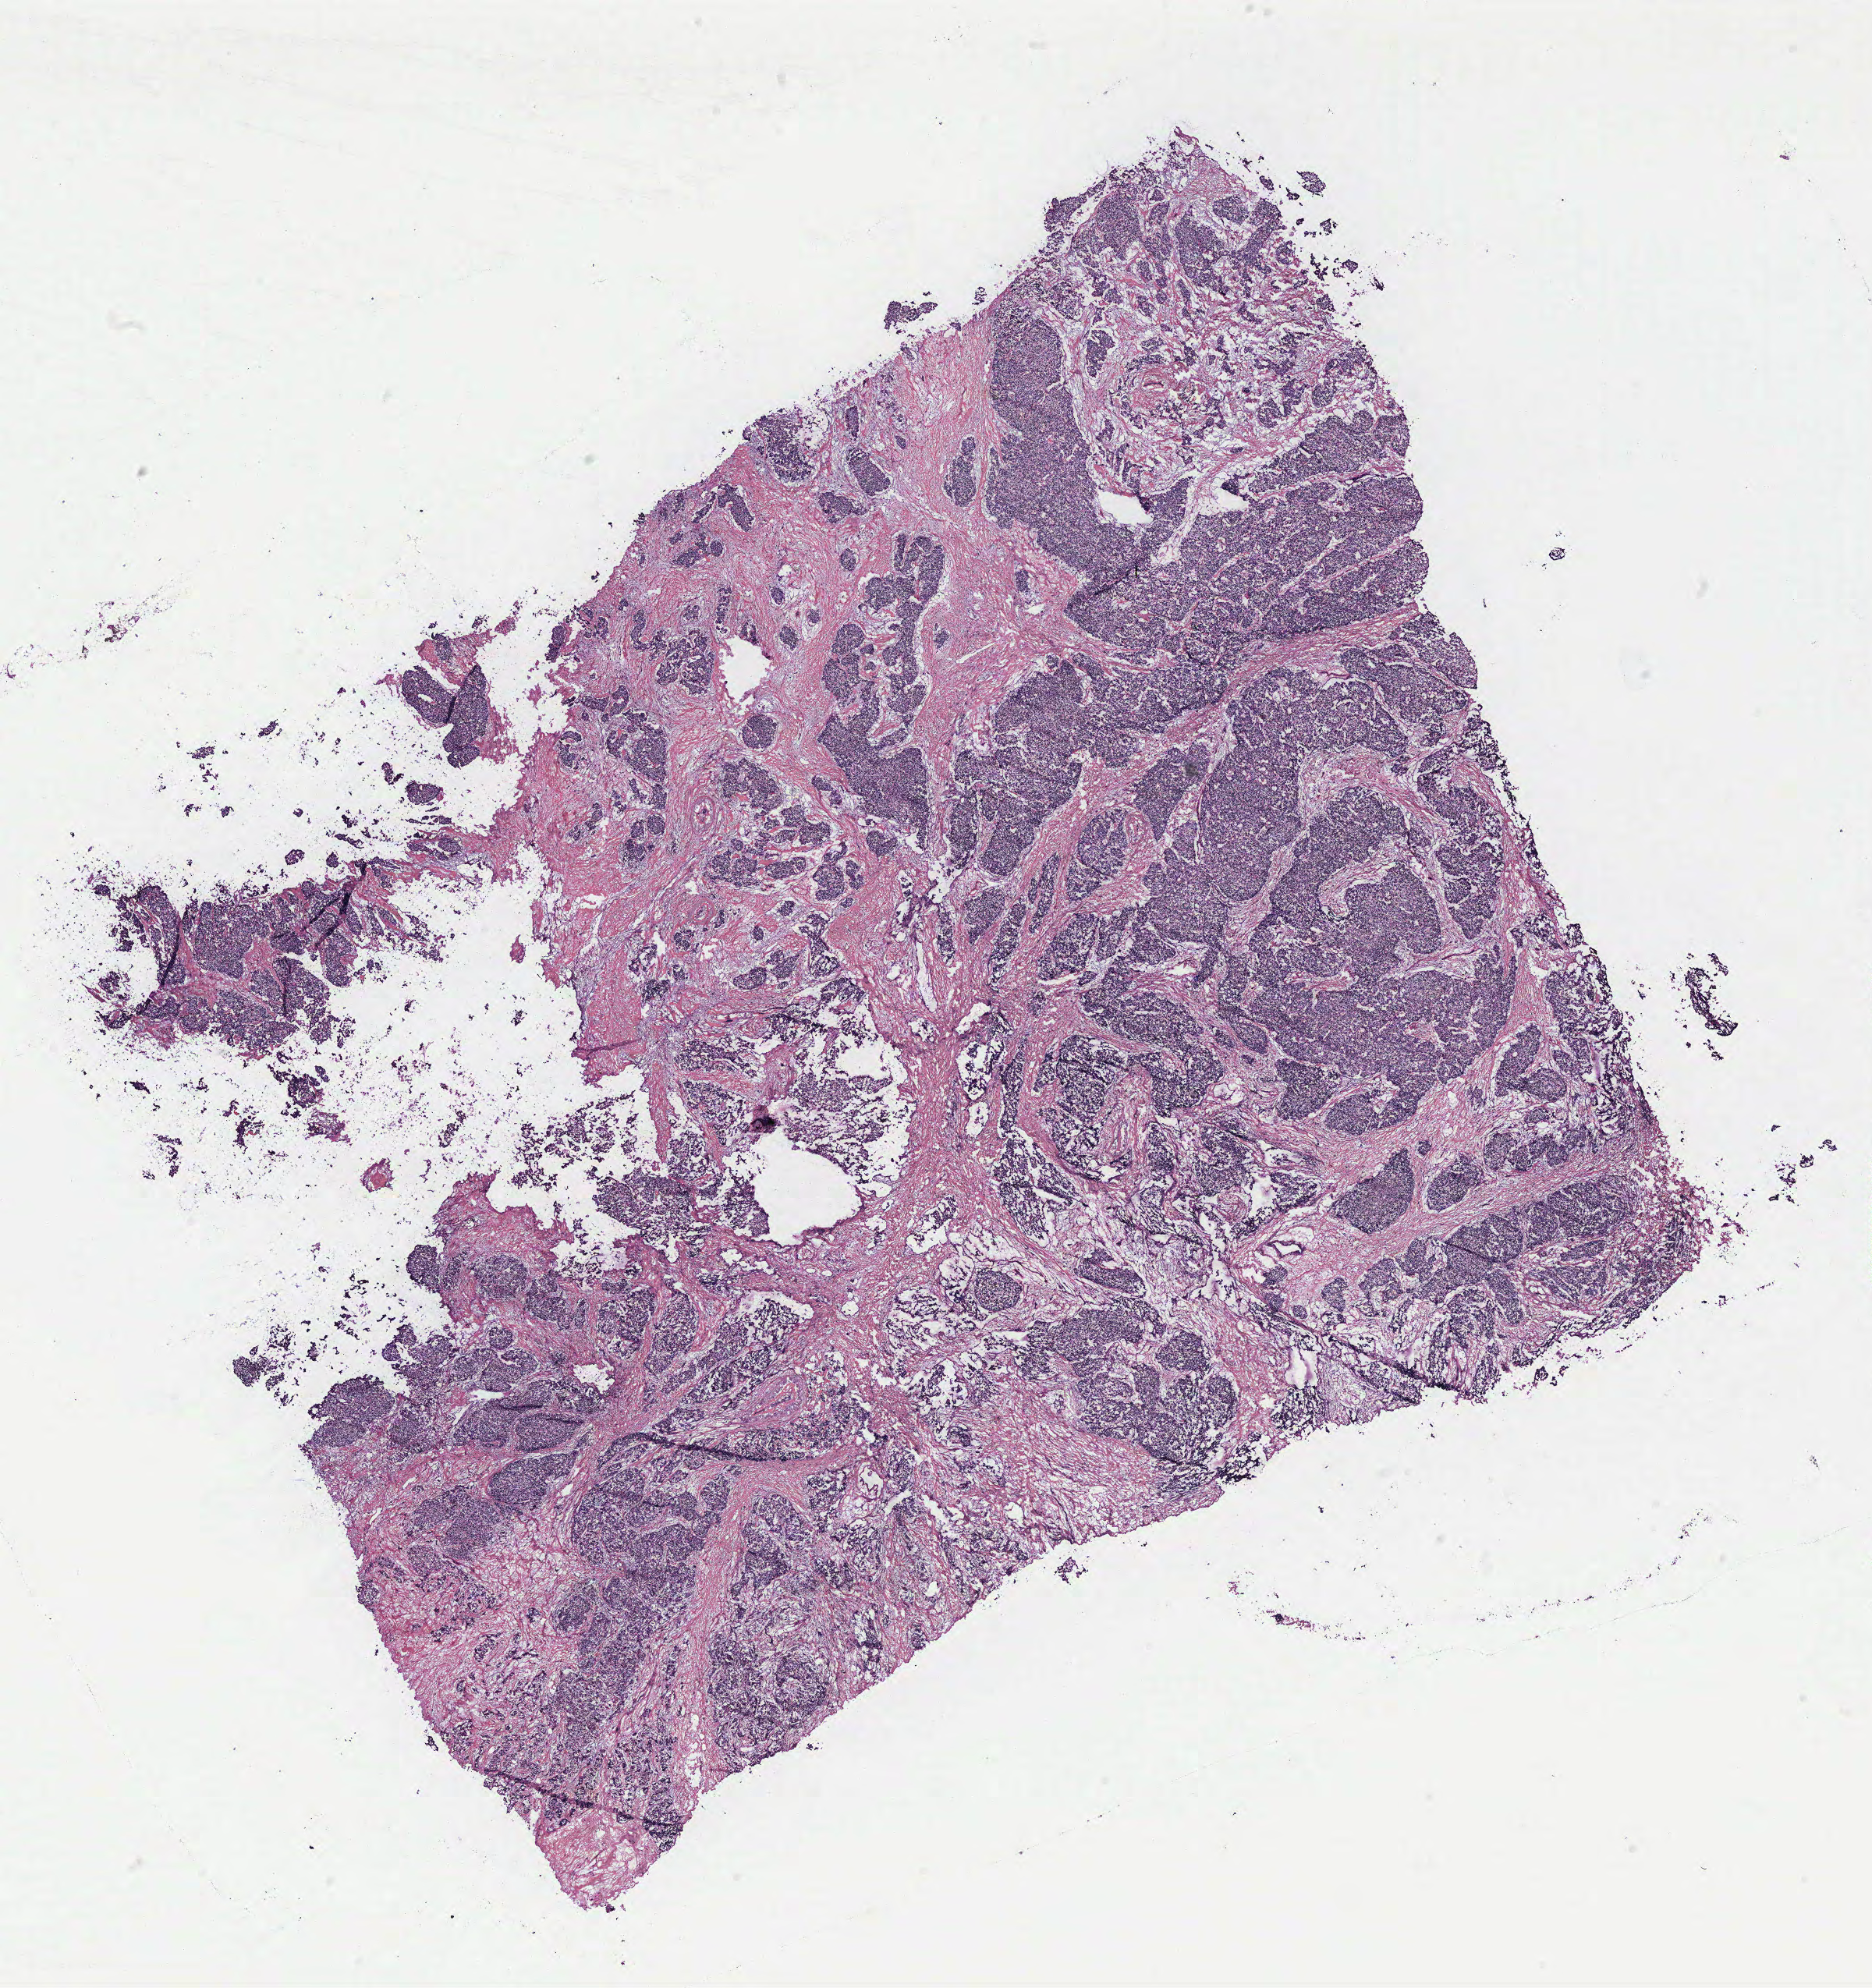
H&E-stained whole-slide image — low-resolution overview of the scanned area, about 19.2 x 20.4 mm (from a 40x scan); breast, tissue type not recorded. Patient: female, age 77 years.
Patient diagnosis: Infiltrating duct carcinoma, NOS.